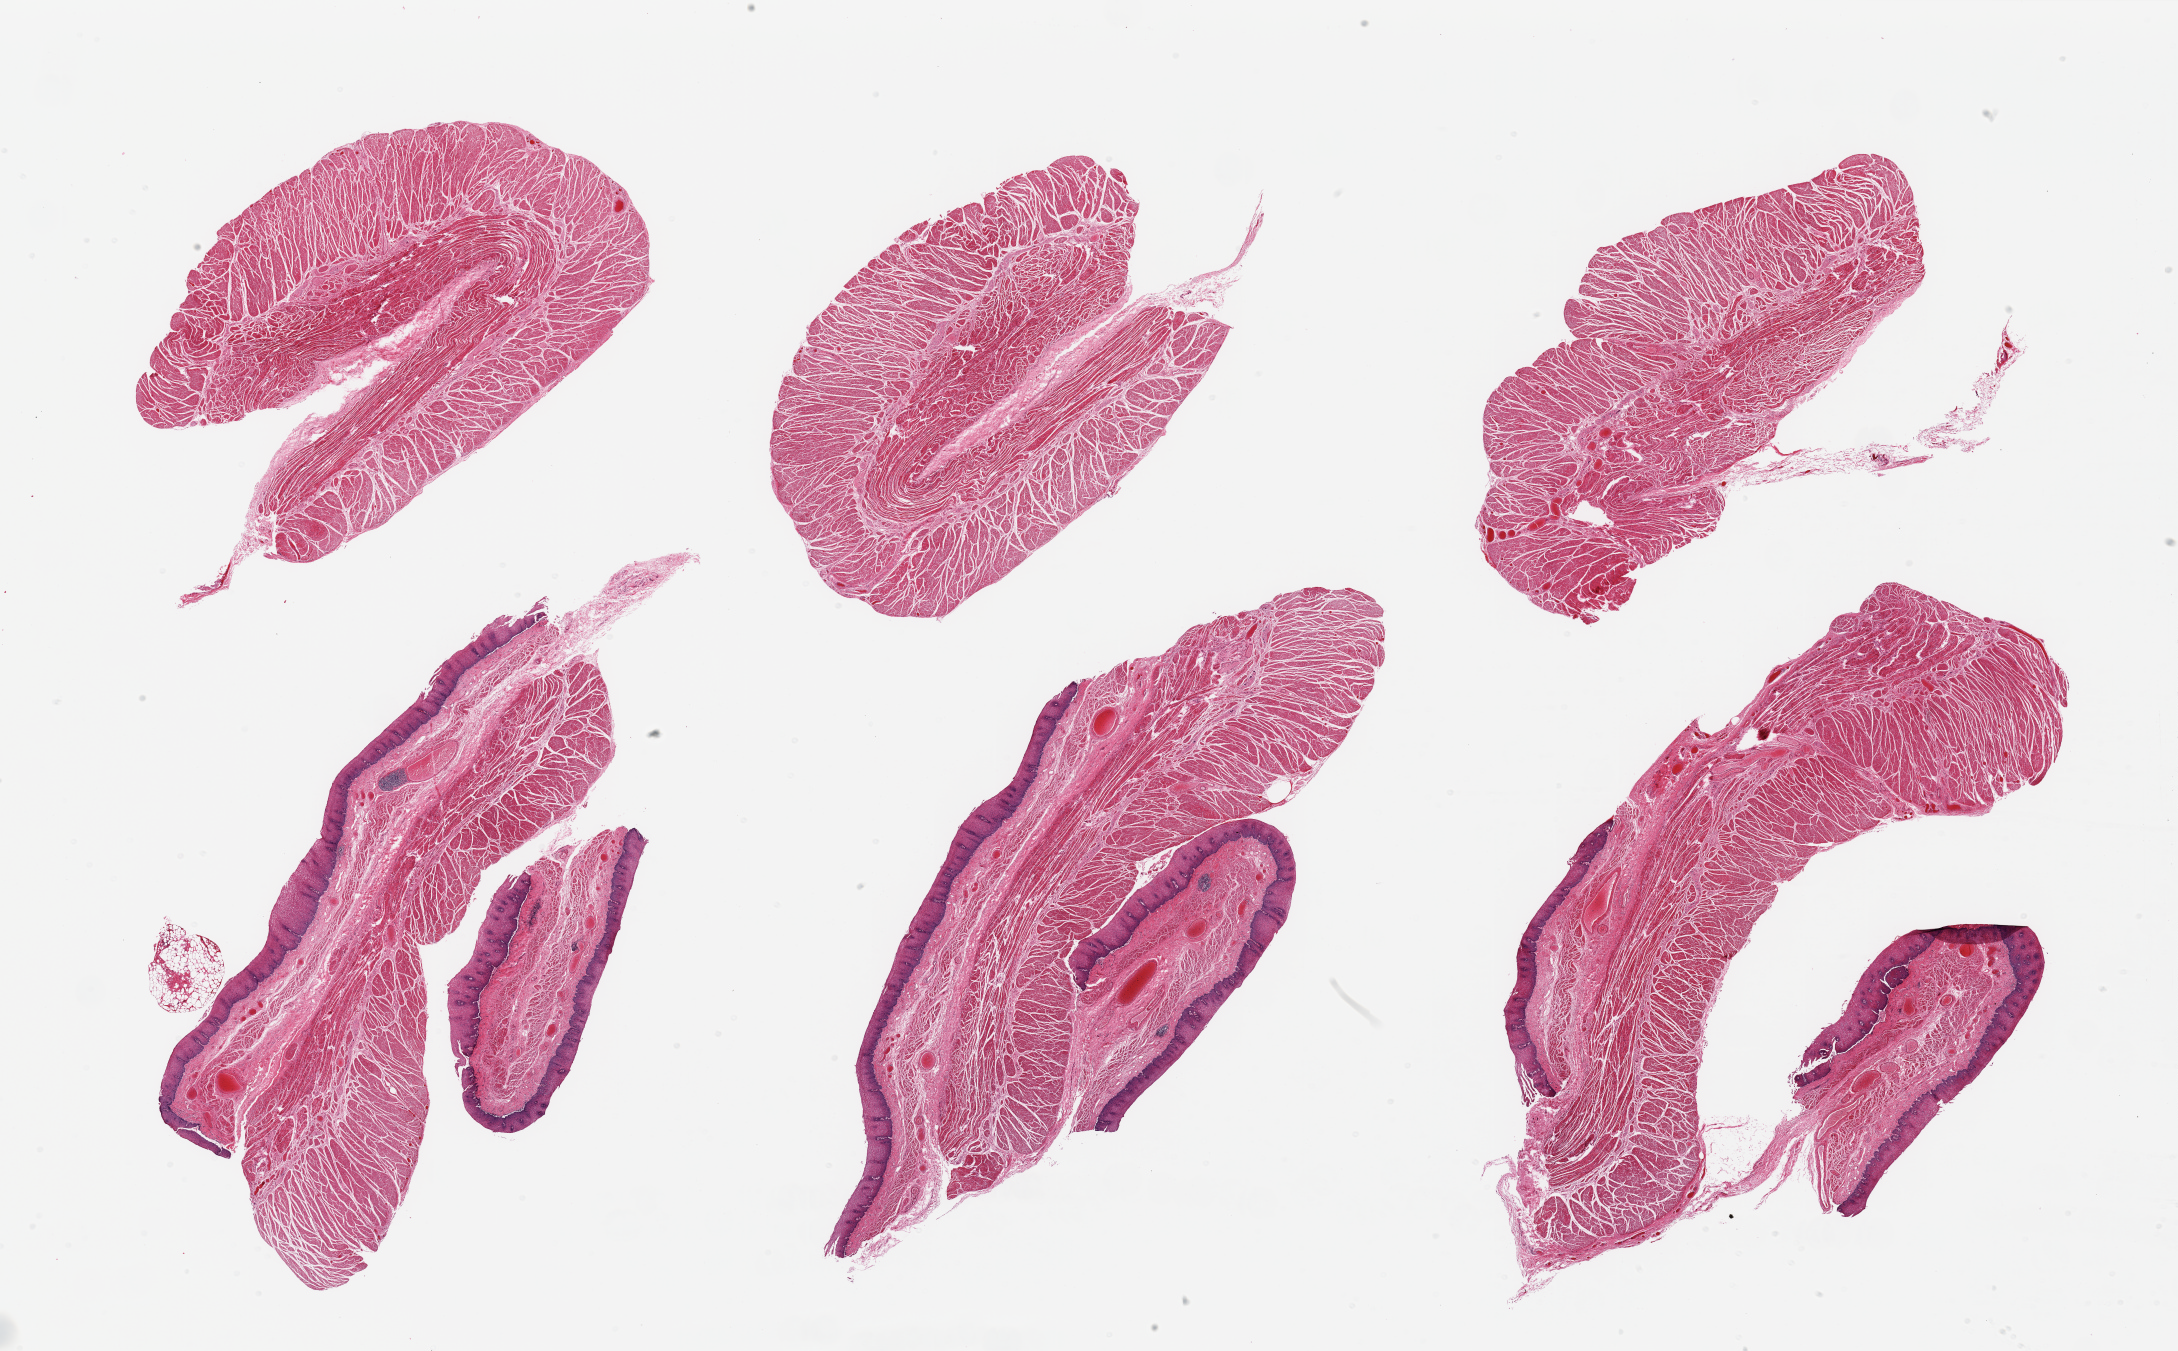
Digitized hematoxylin and eosin (H&E)-stained section — shown as a low-resolution overview of the whole scanned area (about 34.5 x 21.4 mm). PAXgene-fixed, paraffin-embedded tissue. Sampled site (target tissue): gastroesophageal junction. Donor tissue sample. Donor sex: male.
Pathologist's review note for this sample: 6 pieces, confirmed target muscularis; ~10% 'contaminant' squamous mucosa.